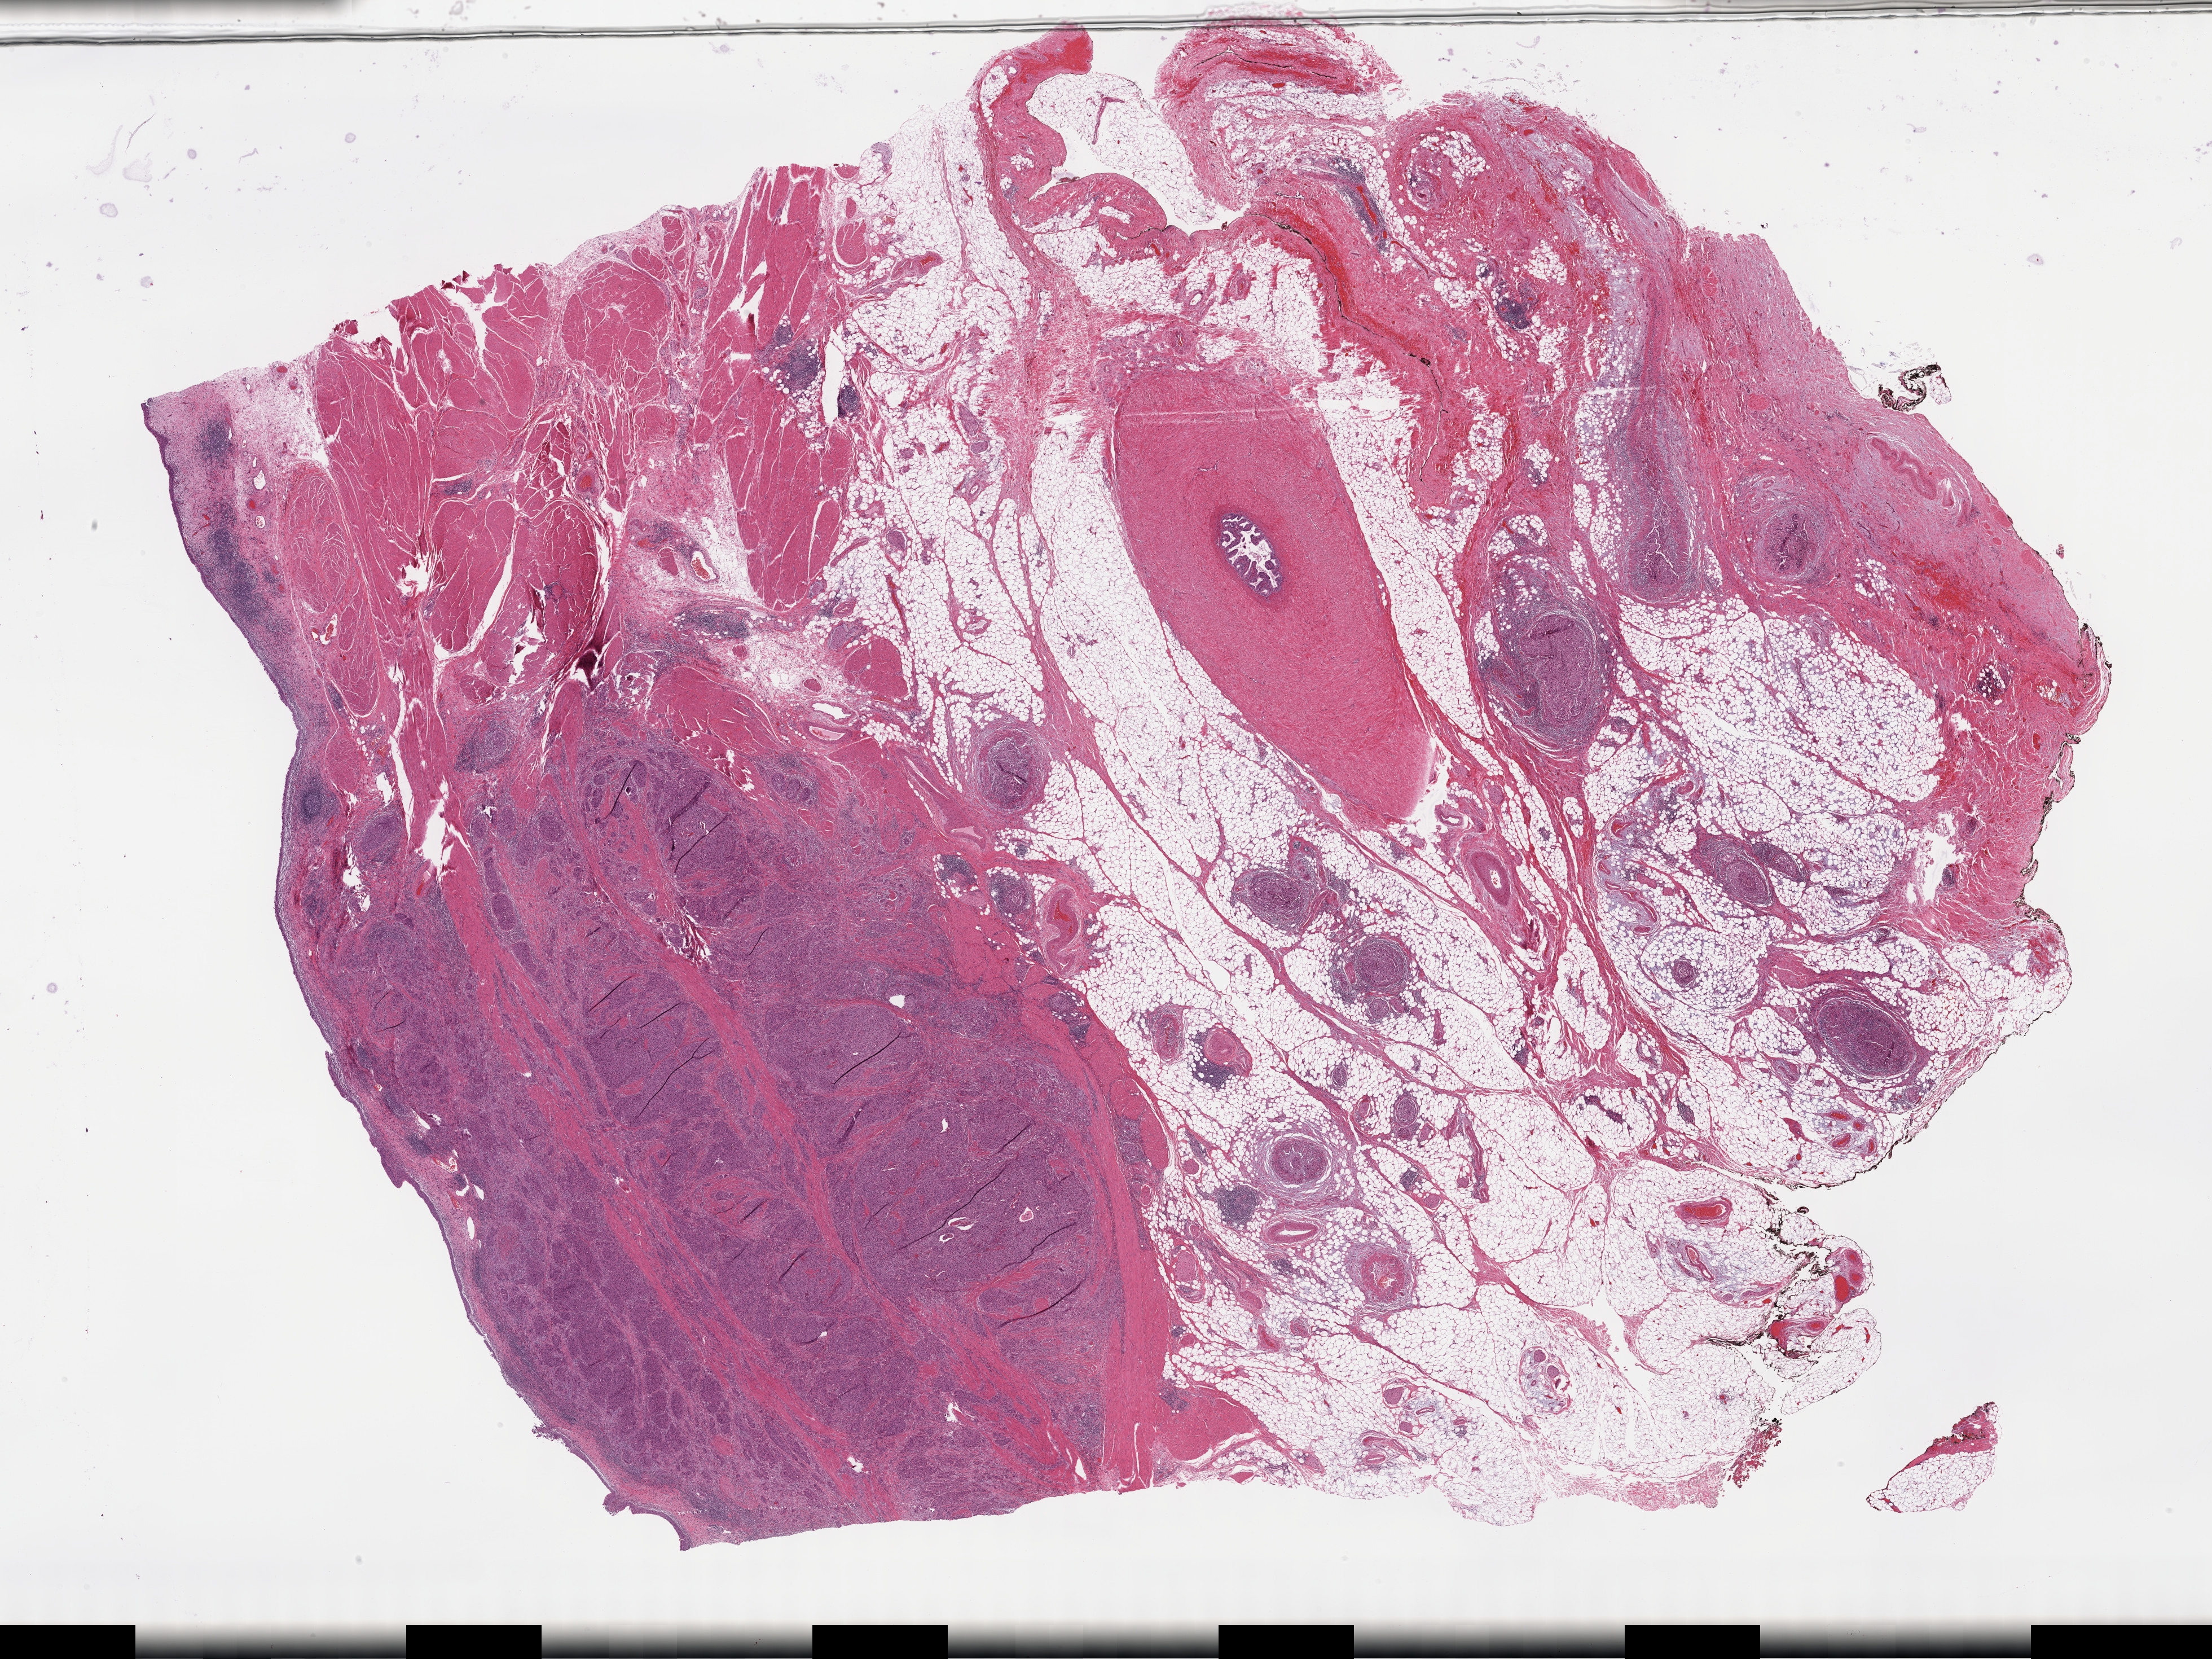
Whole-slide histology image, H&E-stained — low-resolution overview of the scanned area, about 31.7 x 23.8 mm (from a 40x scan); formalin-fixed paraffin-embedded (FFPE) diagnostic section; sample: primary tumour, bladder. Patient: male, age at initial diagnosis 54 years. Histologic grade: high grade.
• AJCC pathologic stage: IV (7th edition)
• histologic diagnosis: Transitional cell carcinoma (trigone of bladder)